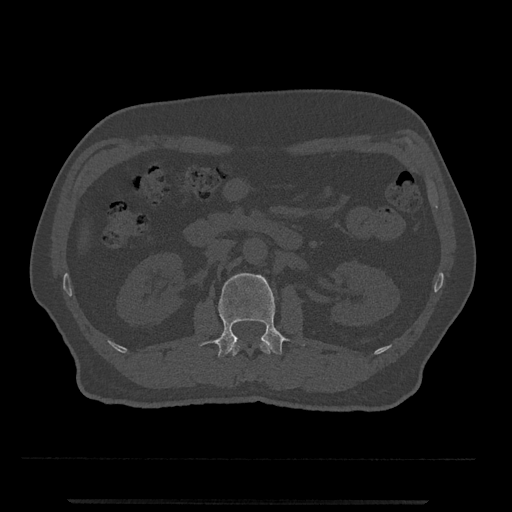
CT including the spine, one axial slice; slice 284 of 797 in the series (ordered by position); reconstruction kernel Br40s/3; bone window (W 1800 / L 400 HU); 0.5 mm slice thickness; 512 × 512 image matrix, field of view 419 × 419 mm. Patient: male, 63 years. From the clinical record (not read from this slice): primary cancer: prostate.
Outlined on this slice (semi-automatically segmented with operator editing):
- L1 vertebra: bounding box [x1, y1, x2, y2] px = [231, 341, 273, 356]
- L2 vertebra: [199, 273, 288, 357]